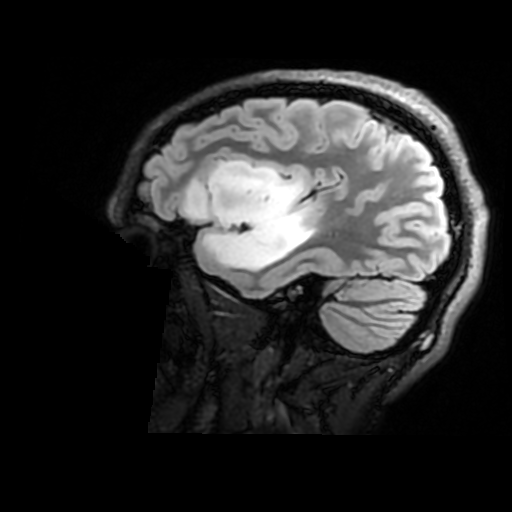
Brain MRI from a brain-tumour surgery series, one sagittal slice; position 128 of 176 along the scan axis; T2 FLAIR; 512 × 512 image matrix. Case-level facts recorded for this patient, not image findings: histopathology: Astrocytoma; WHO grade: 2; IDH mutation: yes.
Annotated regions visible in this slice (outlined manually by an expert reader):
- tumour: bounding box <187,159,315,272> (left, top, right, bottom; pixels)